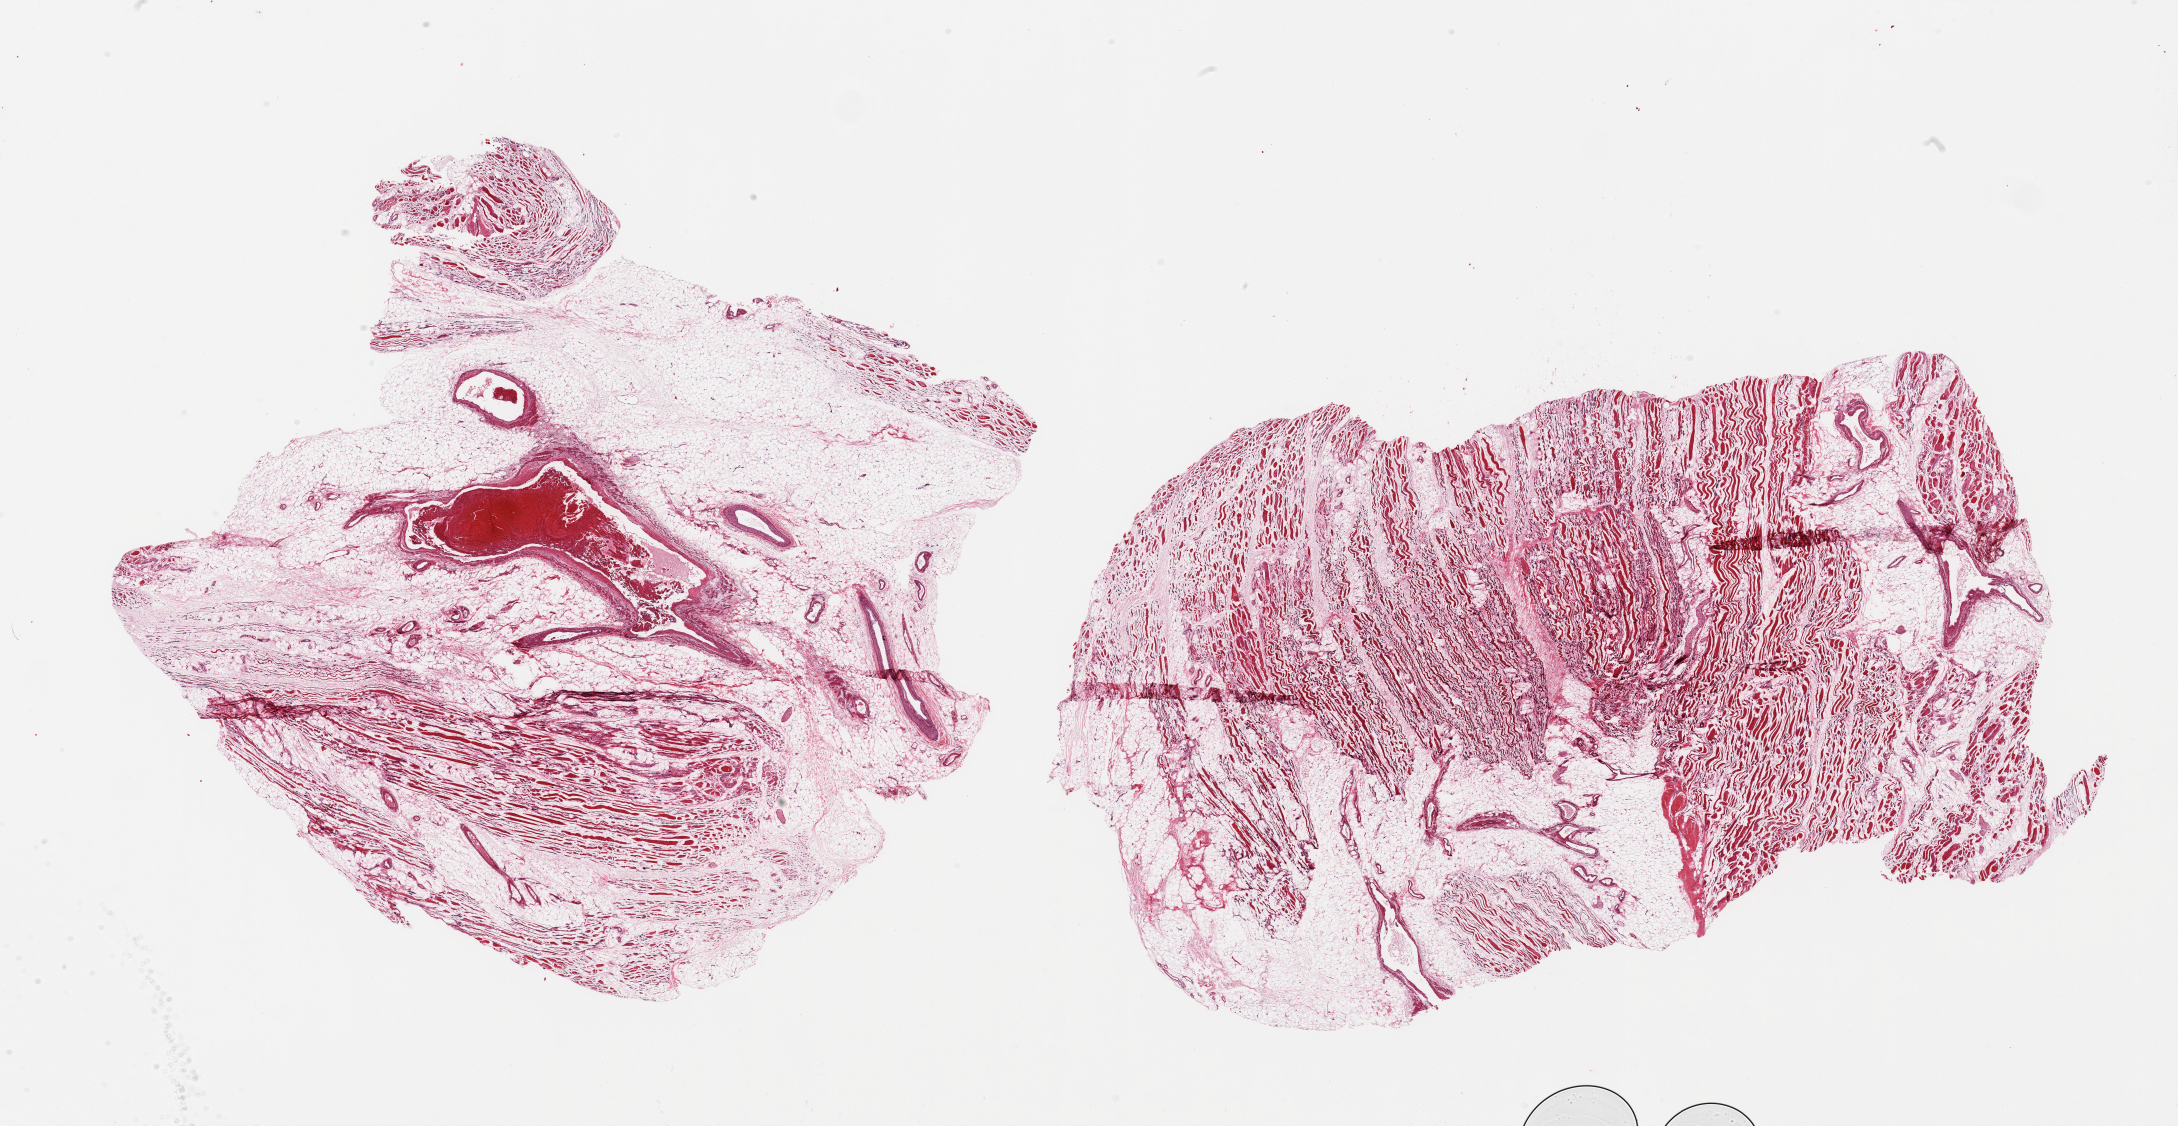
H&E whole-slide image — shown as a low-resolution overview of the whole scanned area (about 34.5 x 17.8 mm, acquisition: 20x scan). PAXgene-fixed paraffin-embedded (PFPE) section. Sampled site (target tissue): skeletal muscle. Tissue donor sample. Donor sex: female.
Pathologist's review note for this sample: 2 pieces, marked fibrillar atrophy; ~50% interstitial fat/vascular elements.